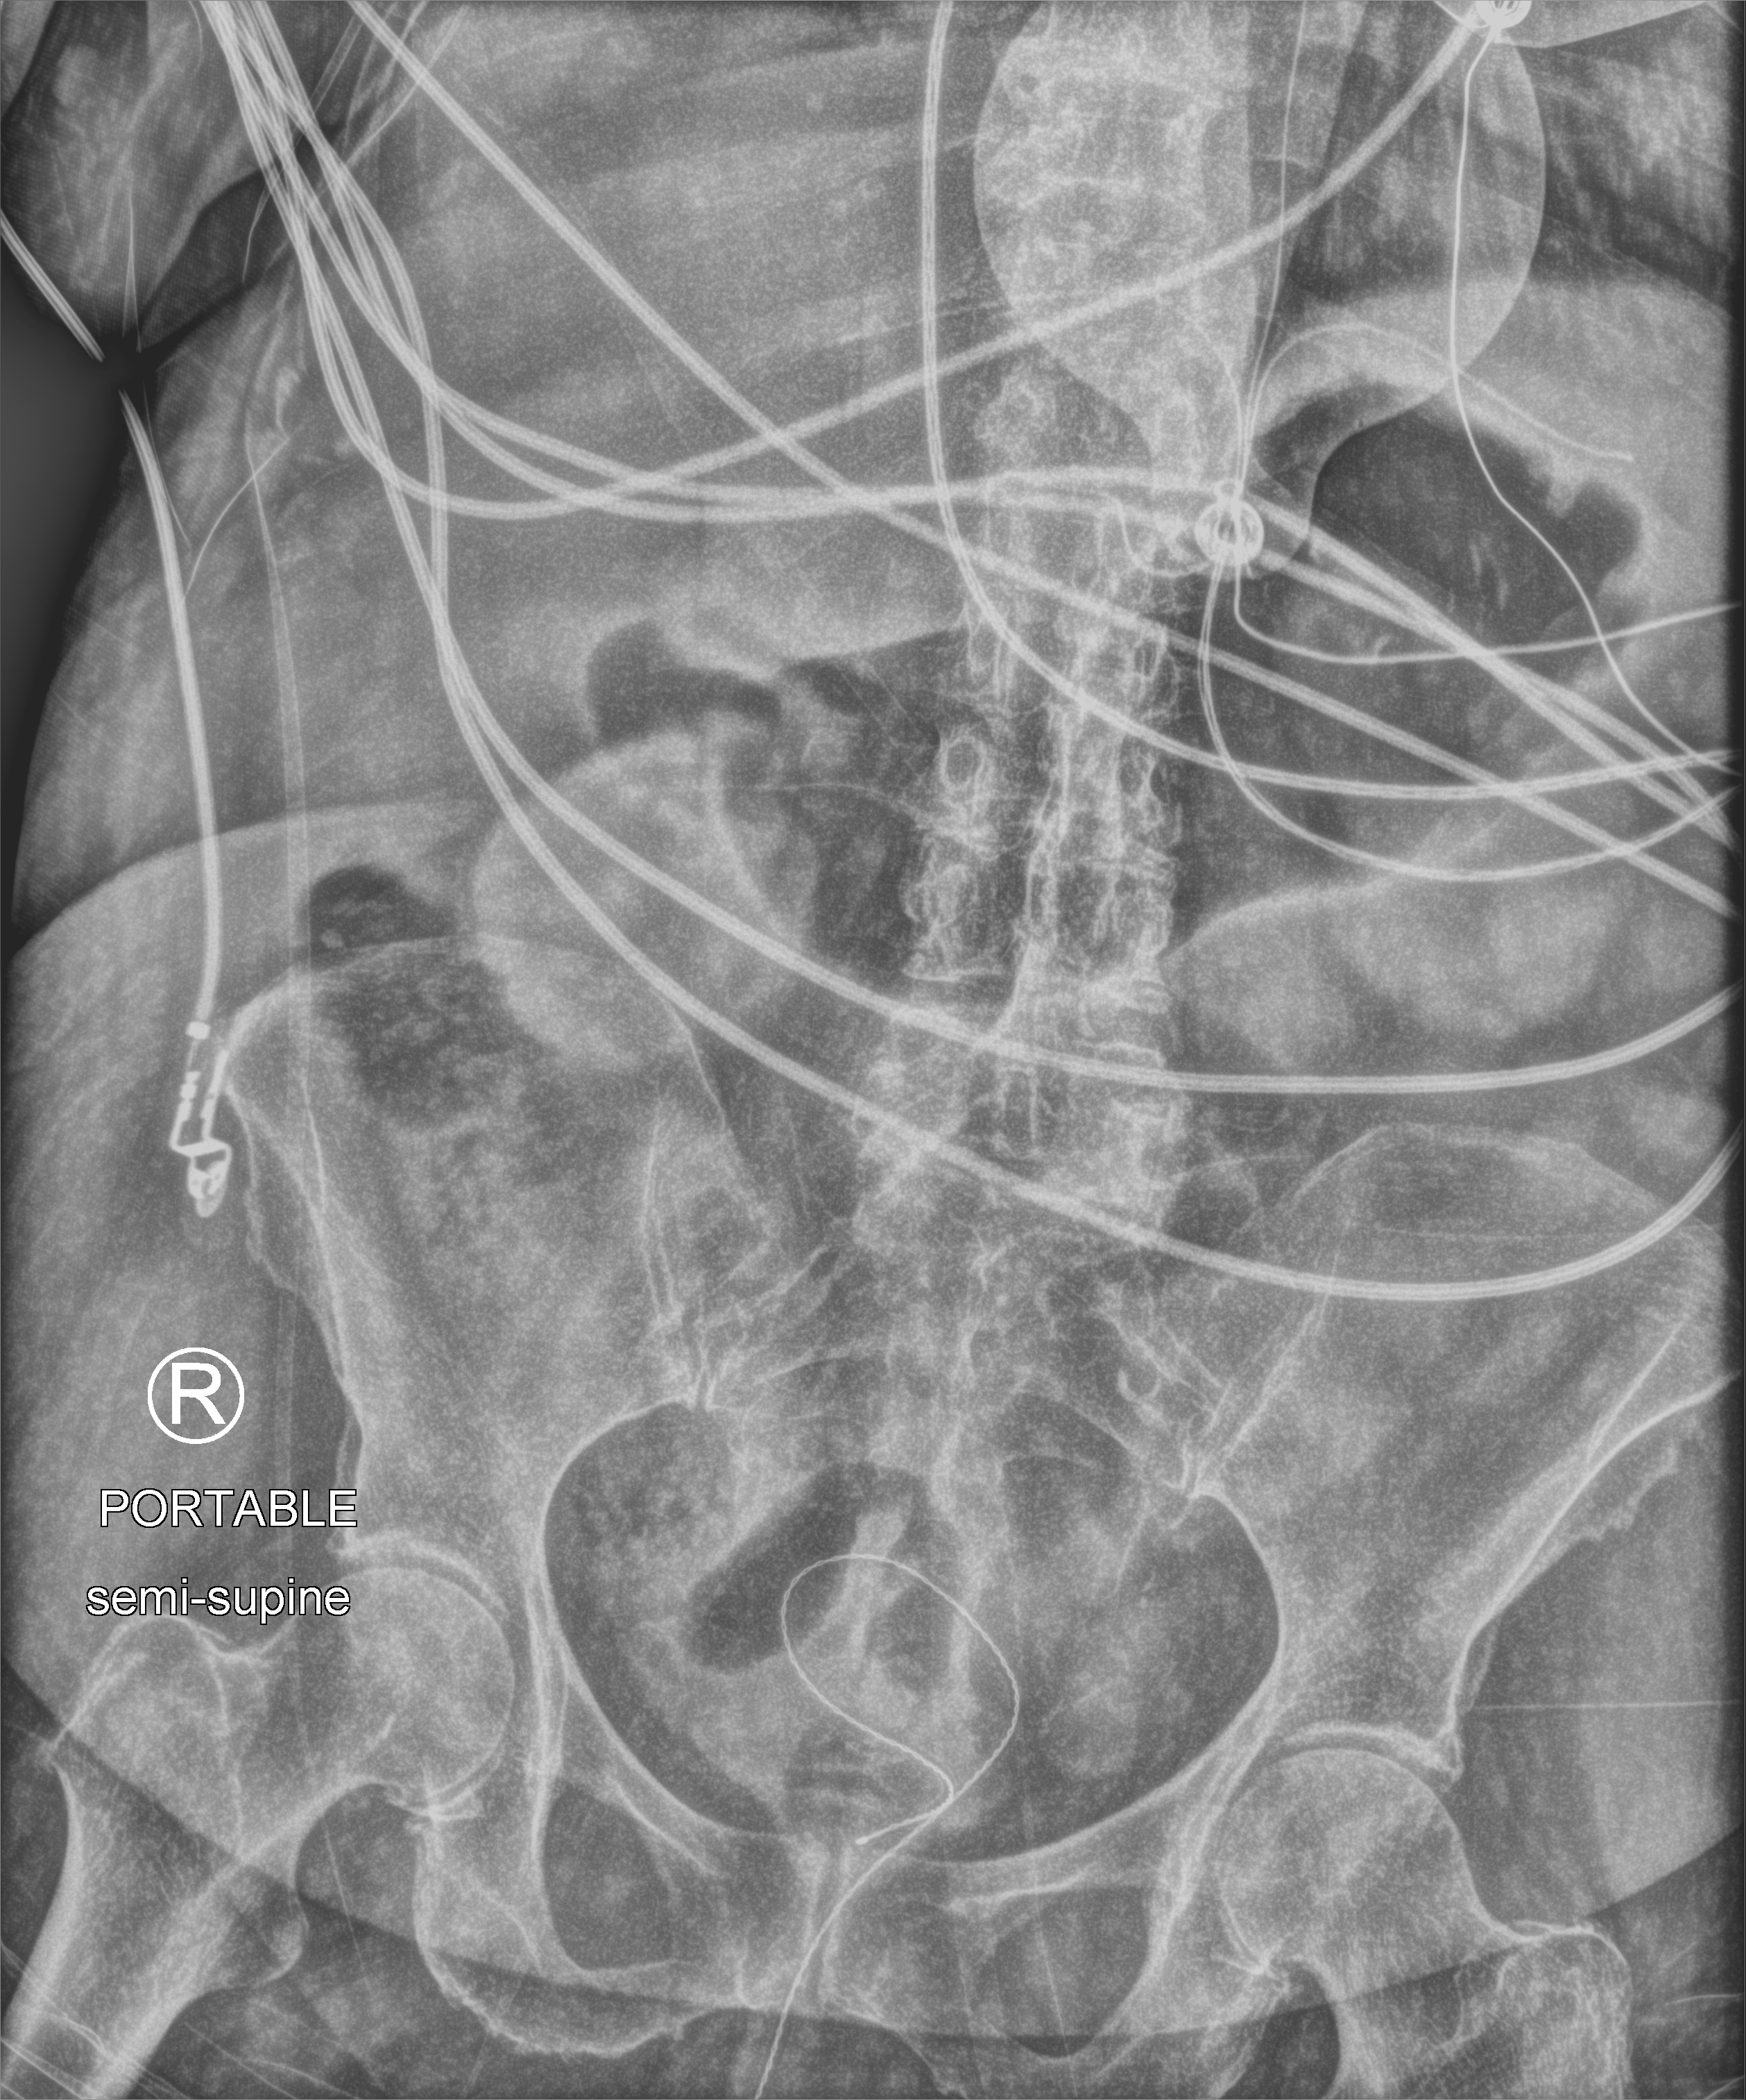
Portable abdomen radiograph; anteroposterior (AP) projection. Patient hospitalised with COVID-19; female, aged 75–90 years.
From the hospital-stay record, not from the radiograph (when in the stay this image was taken is not recorded): admitted to intensive care during this hospital stay: yes; diabetes (admission record): no; other chronic lung disease (admission record): no.